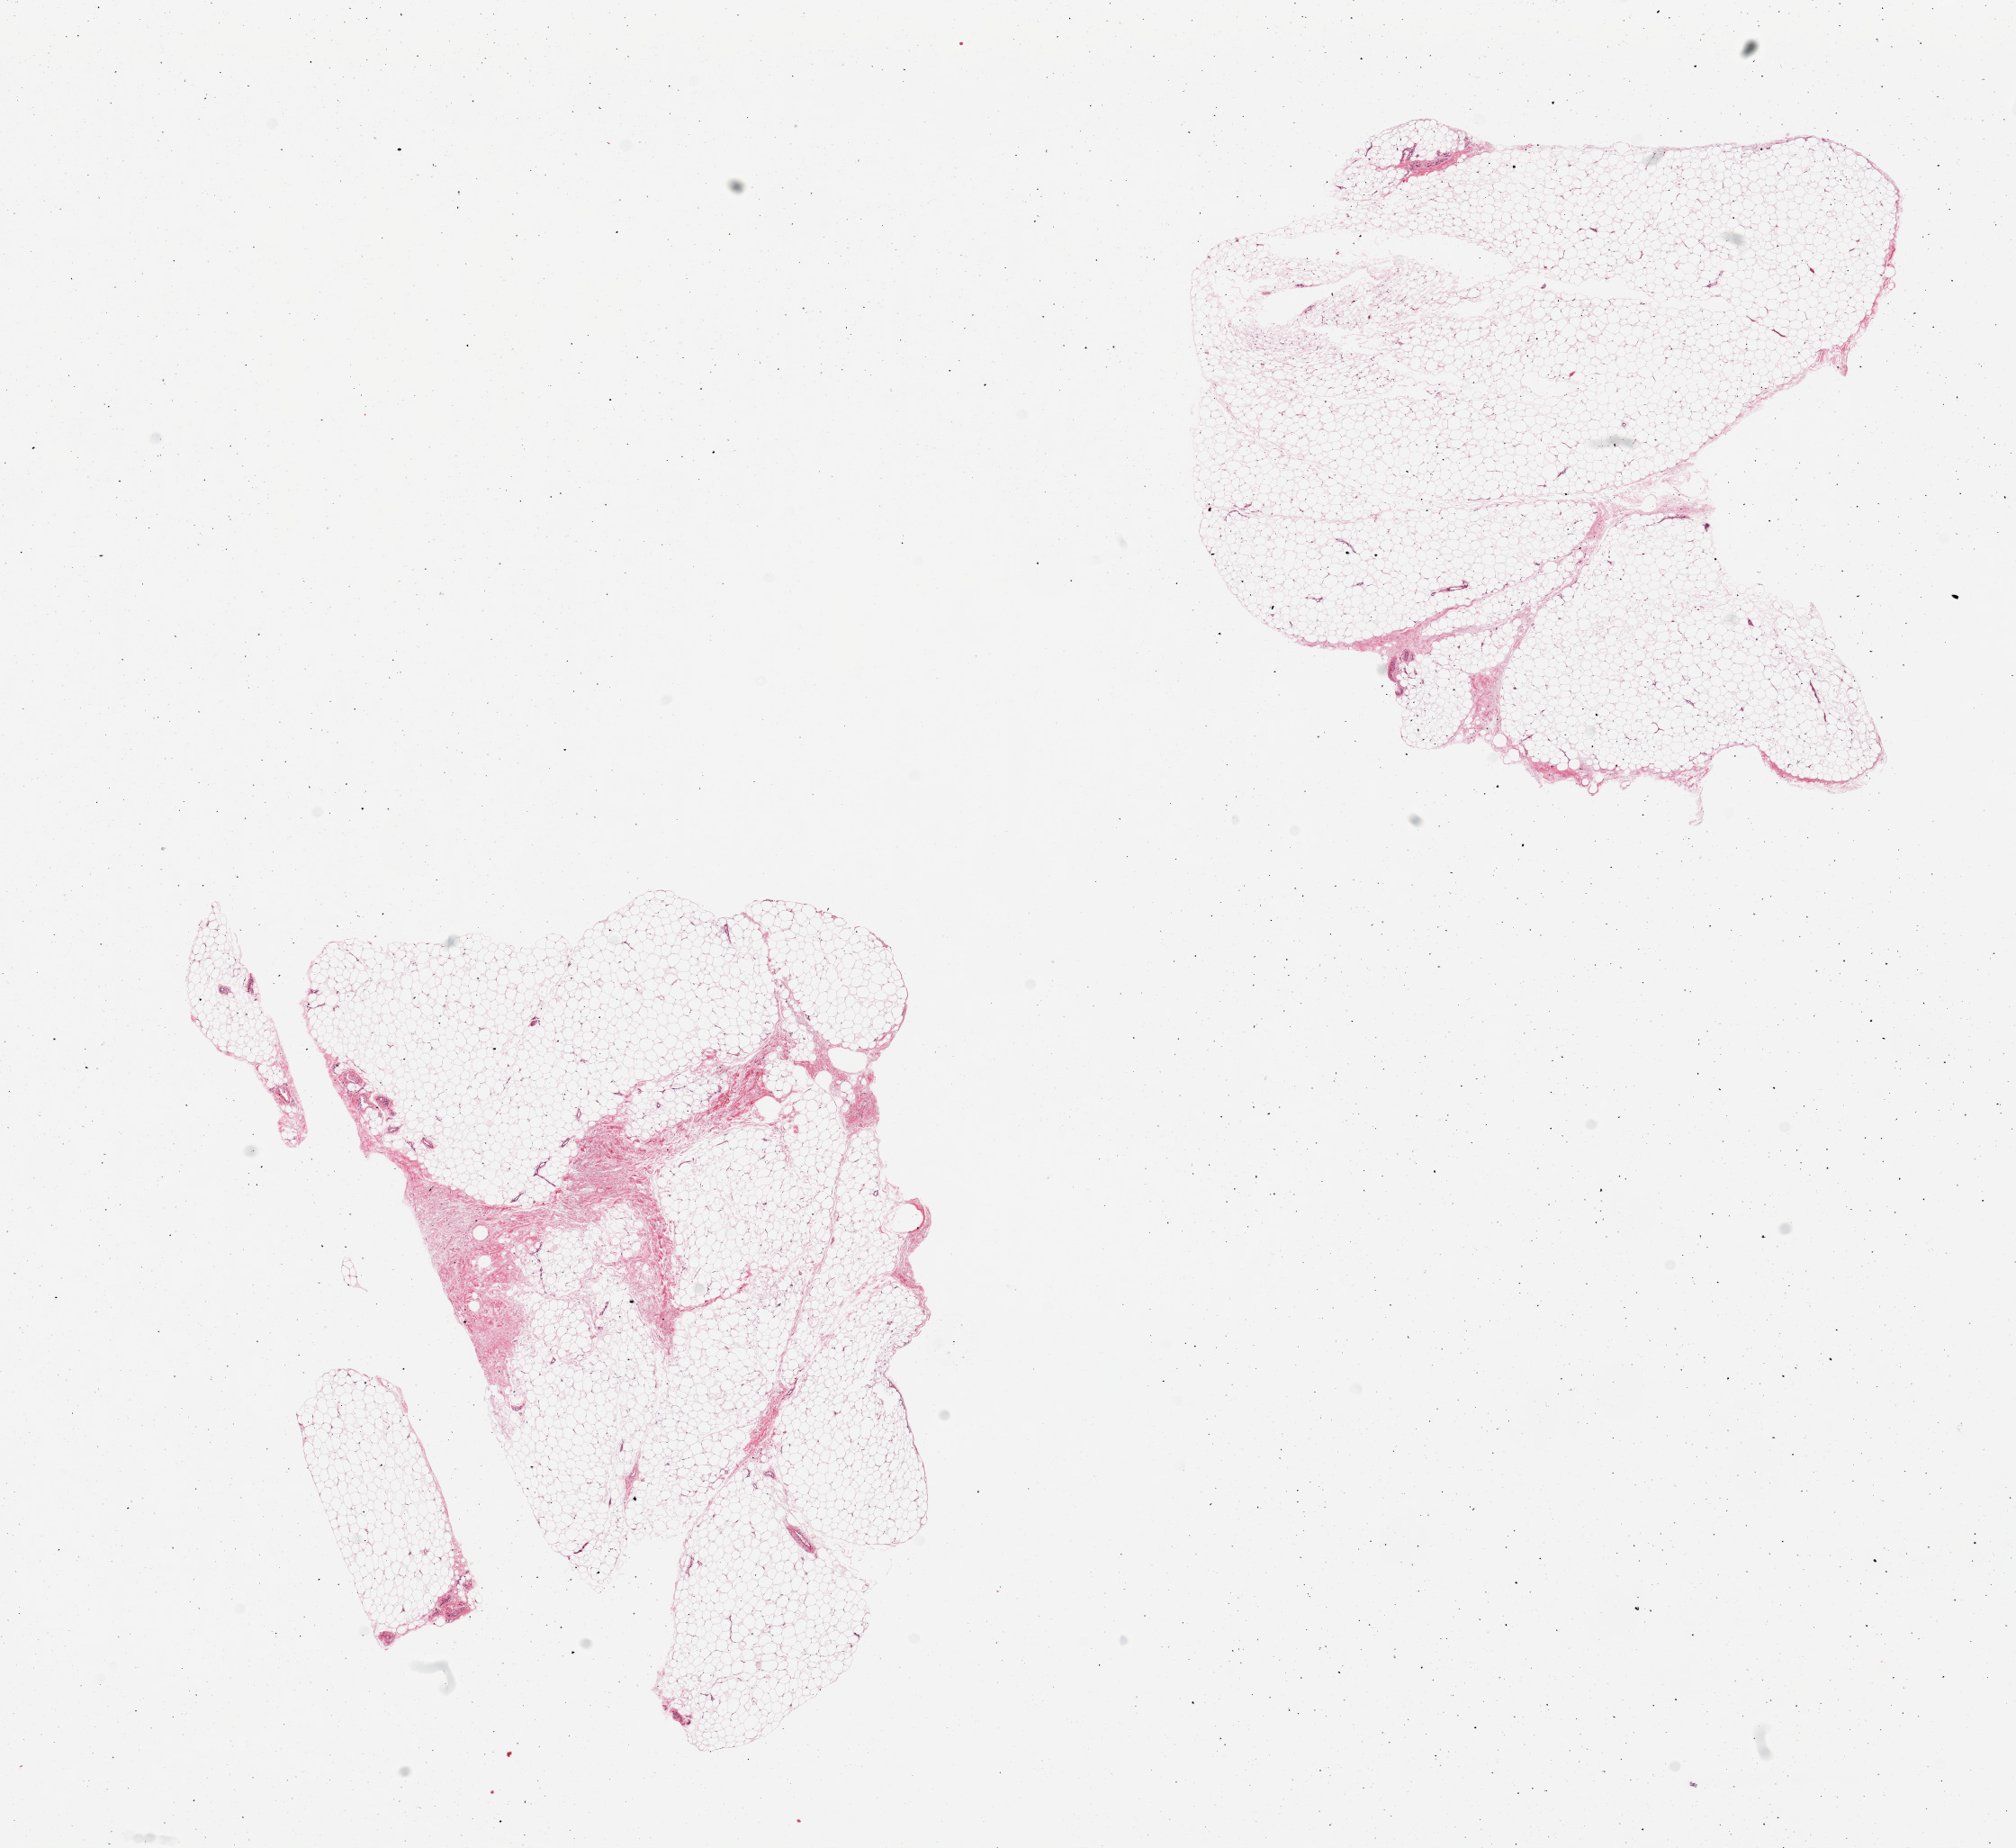
Whole-slide image, hematoxylin and eosin (H&E) stain, brightfield, shown as a low-resolution overview of the whole scanned area (about 17.7 x 16.2 mm); PAXgene-fixed, paraffin-embedded tissue; sampled site (target tissue): adipose tissue; tissue donor sample. Donor sex: female.
- reviewer comment on this tissue sample: 2 pieces; 5% fibrous content